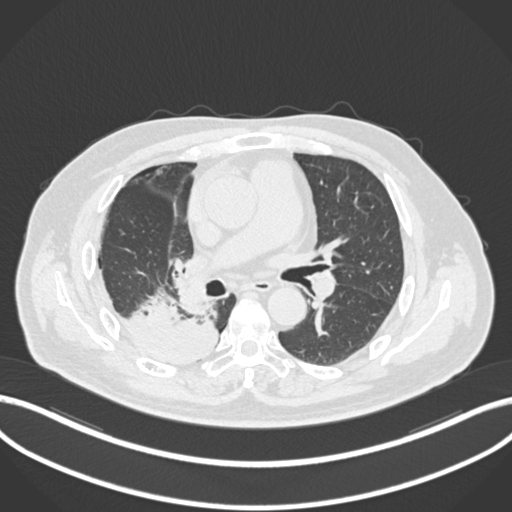
Chest CT, one axial slice; slice 103 of 218 in the series (ordered by position); reconstruction kernel B30f; lung window (W 1500 / L -600 HU); 1 mm slice thickness; 512 × 512 image matrix. Patient: male, 68 years. From the clinical record (not read from this slice): clinical TNM (as recorded): T2a N0 M0.
Outlined on this slice (bounding box drawn by a radiologist):
- lung tumour (recorded histology: adenocarcinoma): bounding box <118,286,218,369> (left, top, right, bottom; pixels)